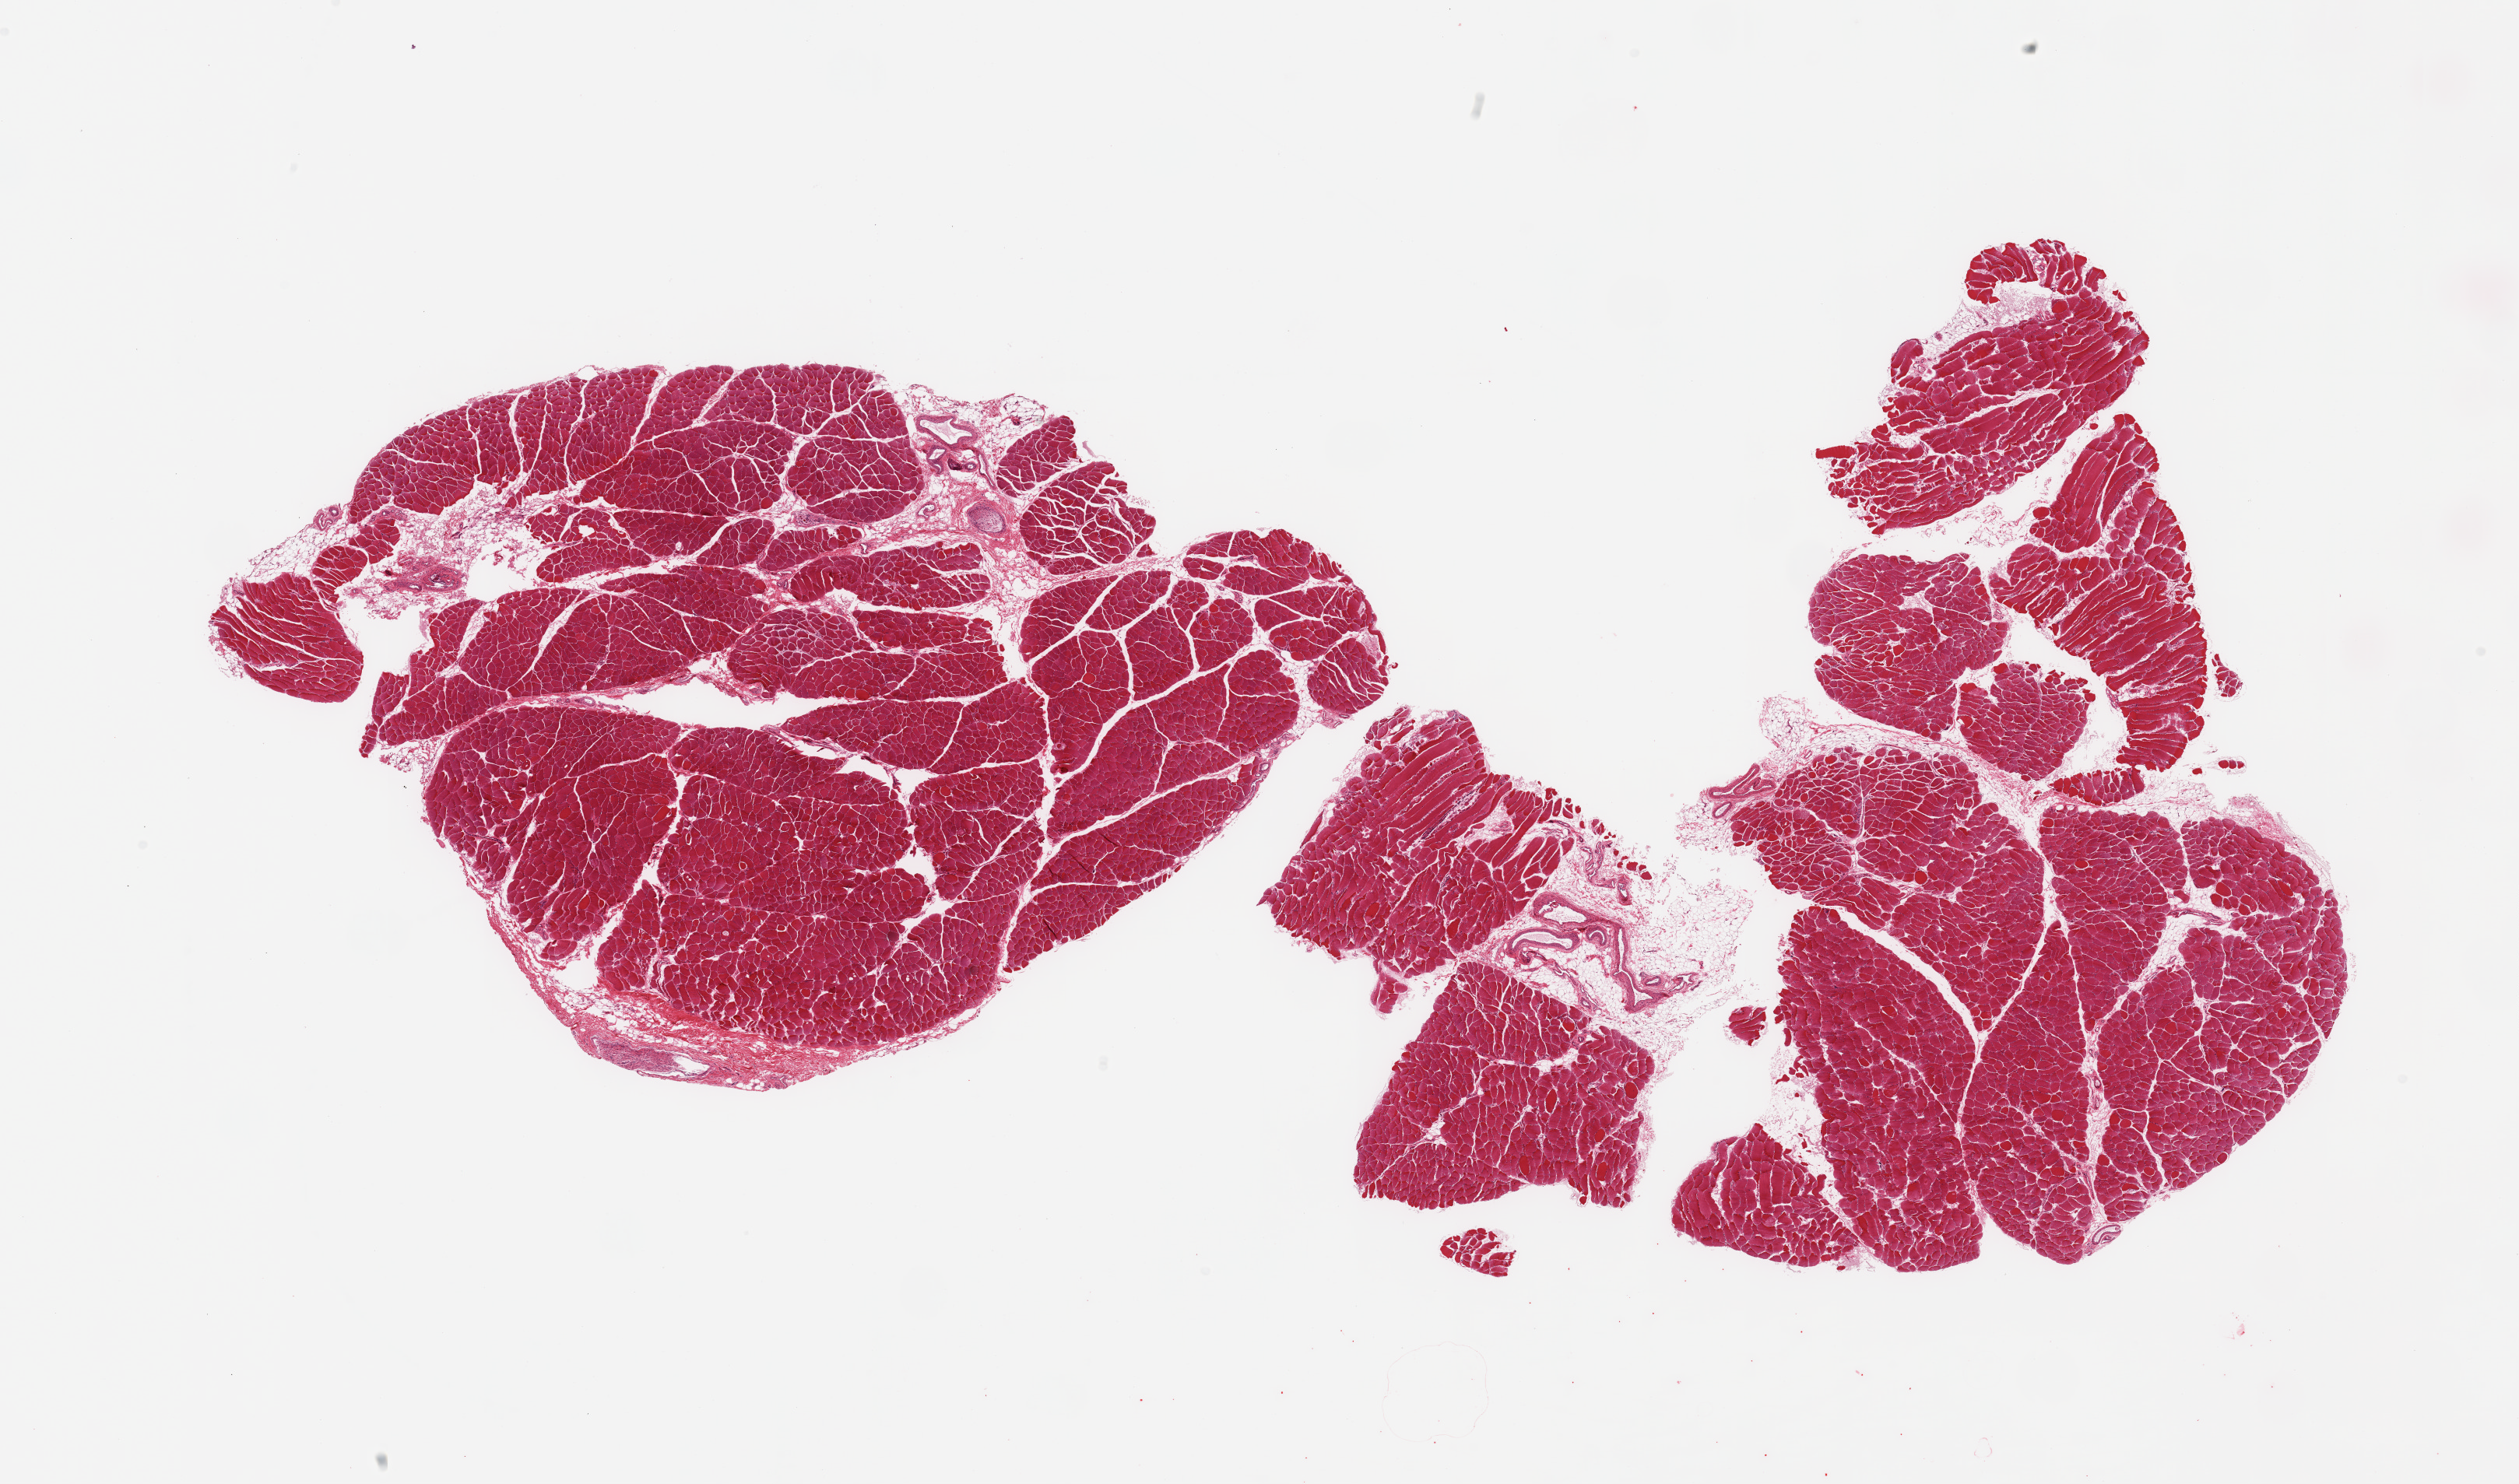
Haematoxylin and eosin whole-slide image, low-resolution overview of the scanned area, about 25.6 x 15.1 mm (from a 20x scan), PAXgene-fixed, paraffin-embedded tissue, section of skeletal muscle (target tissue), tissue donor sample. Donor sex: male.
Reviewer comment on this tissue sample: 2 pieces; ~10% internal fat and nerve.